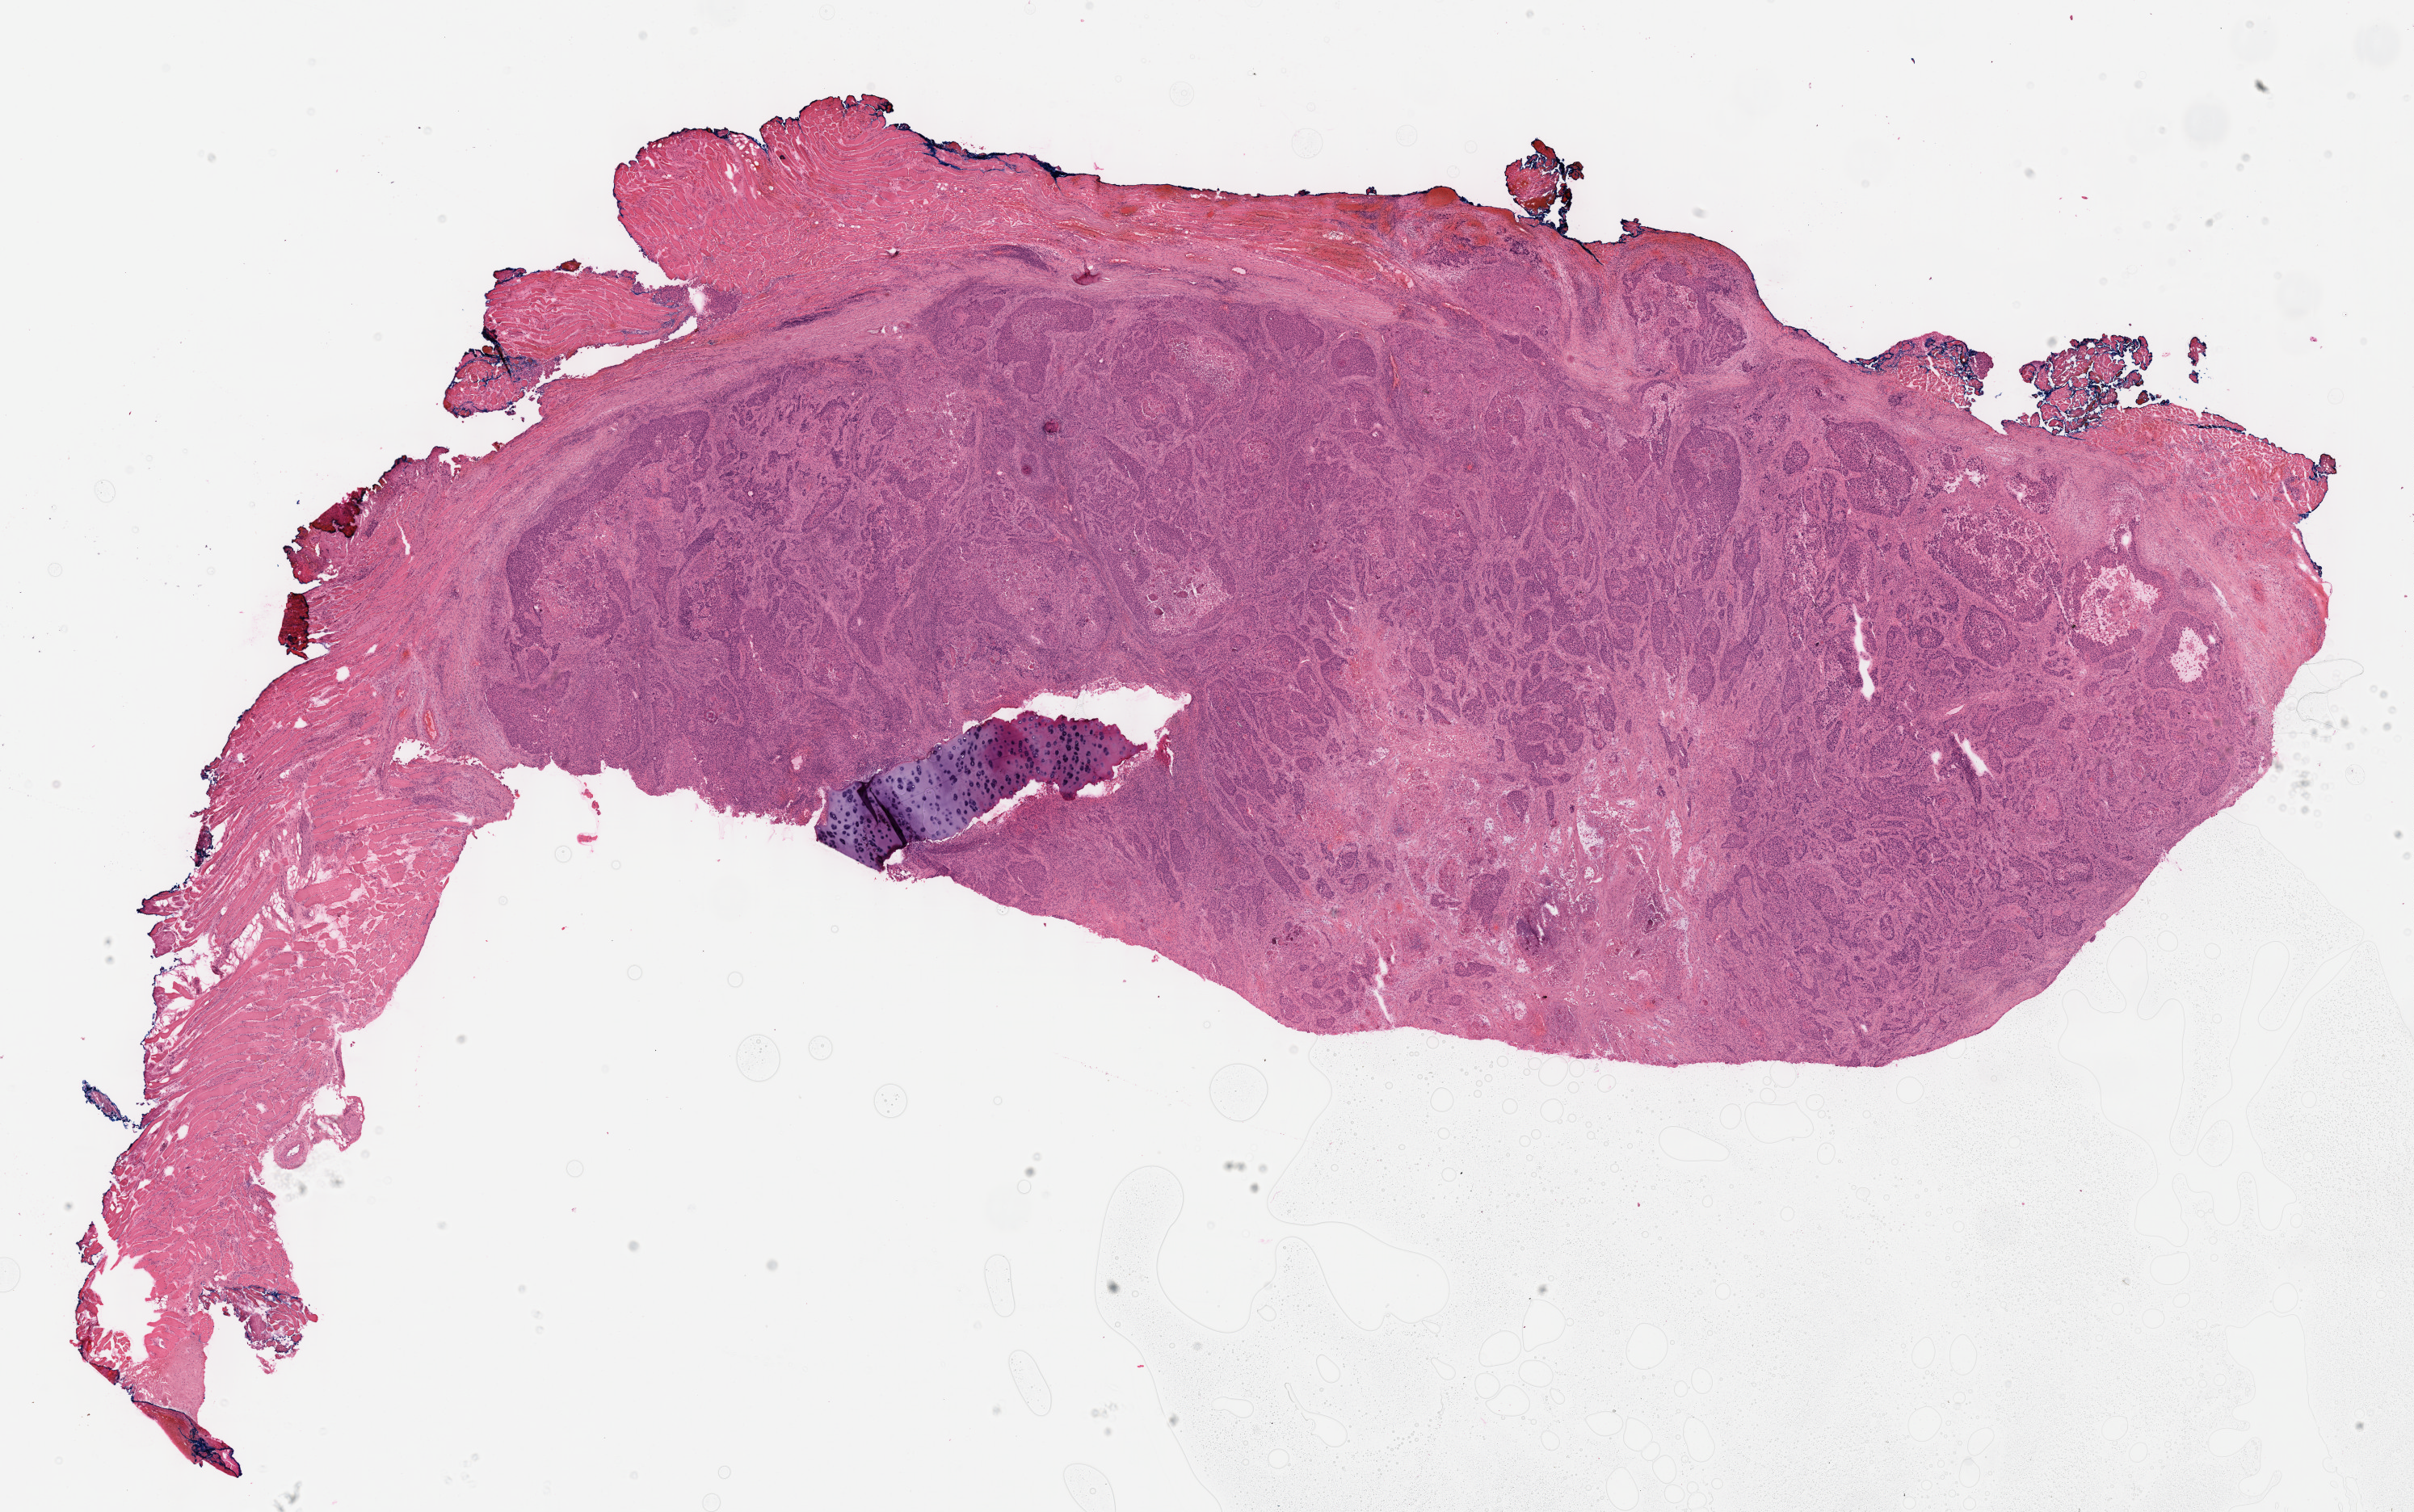
Digitized H&E tissue section (whole slide) — a low-resolution overview of the entire scanned area, about 24.1 x 15.1 mm, formalin-fixed paraffin-embedded (FFPE) diagnostic section, primary tumour sample from the head and neck. Patient: male, age at initial diagnosis 55 years. Histologic grade: G3 (poorly differentiated).
• laterality: right
• pathologic diagnosis: Squamous cell carcinoma, NOS (overlapping lesion of lip, oral cavity and pharynx)
• AJCC pathologic stage: II